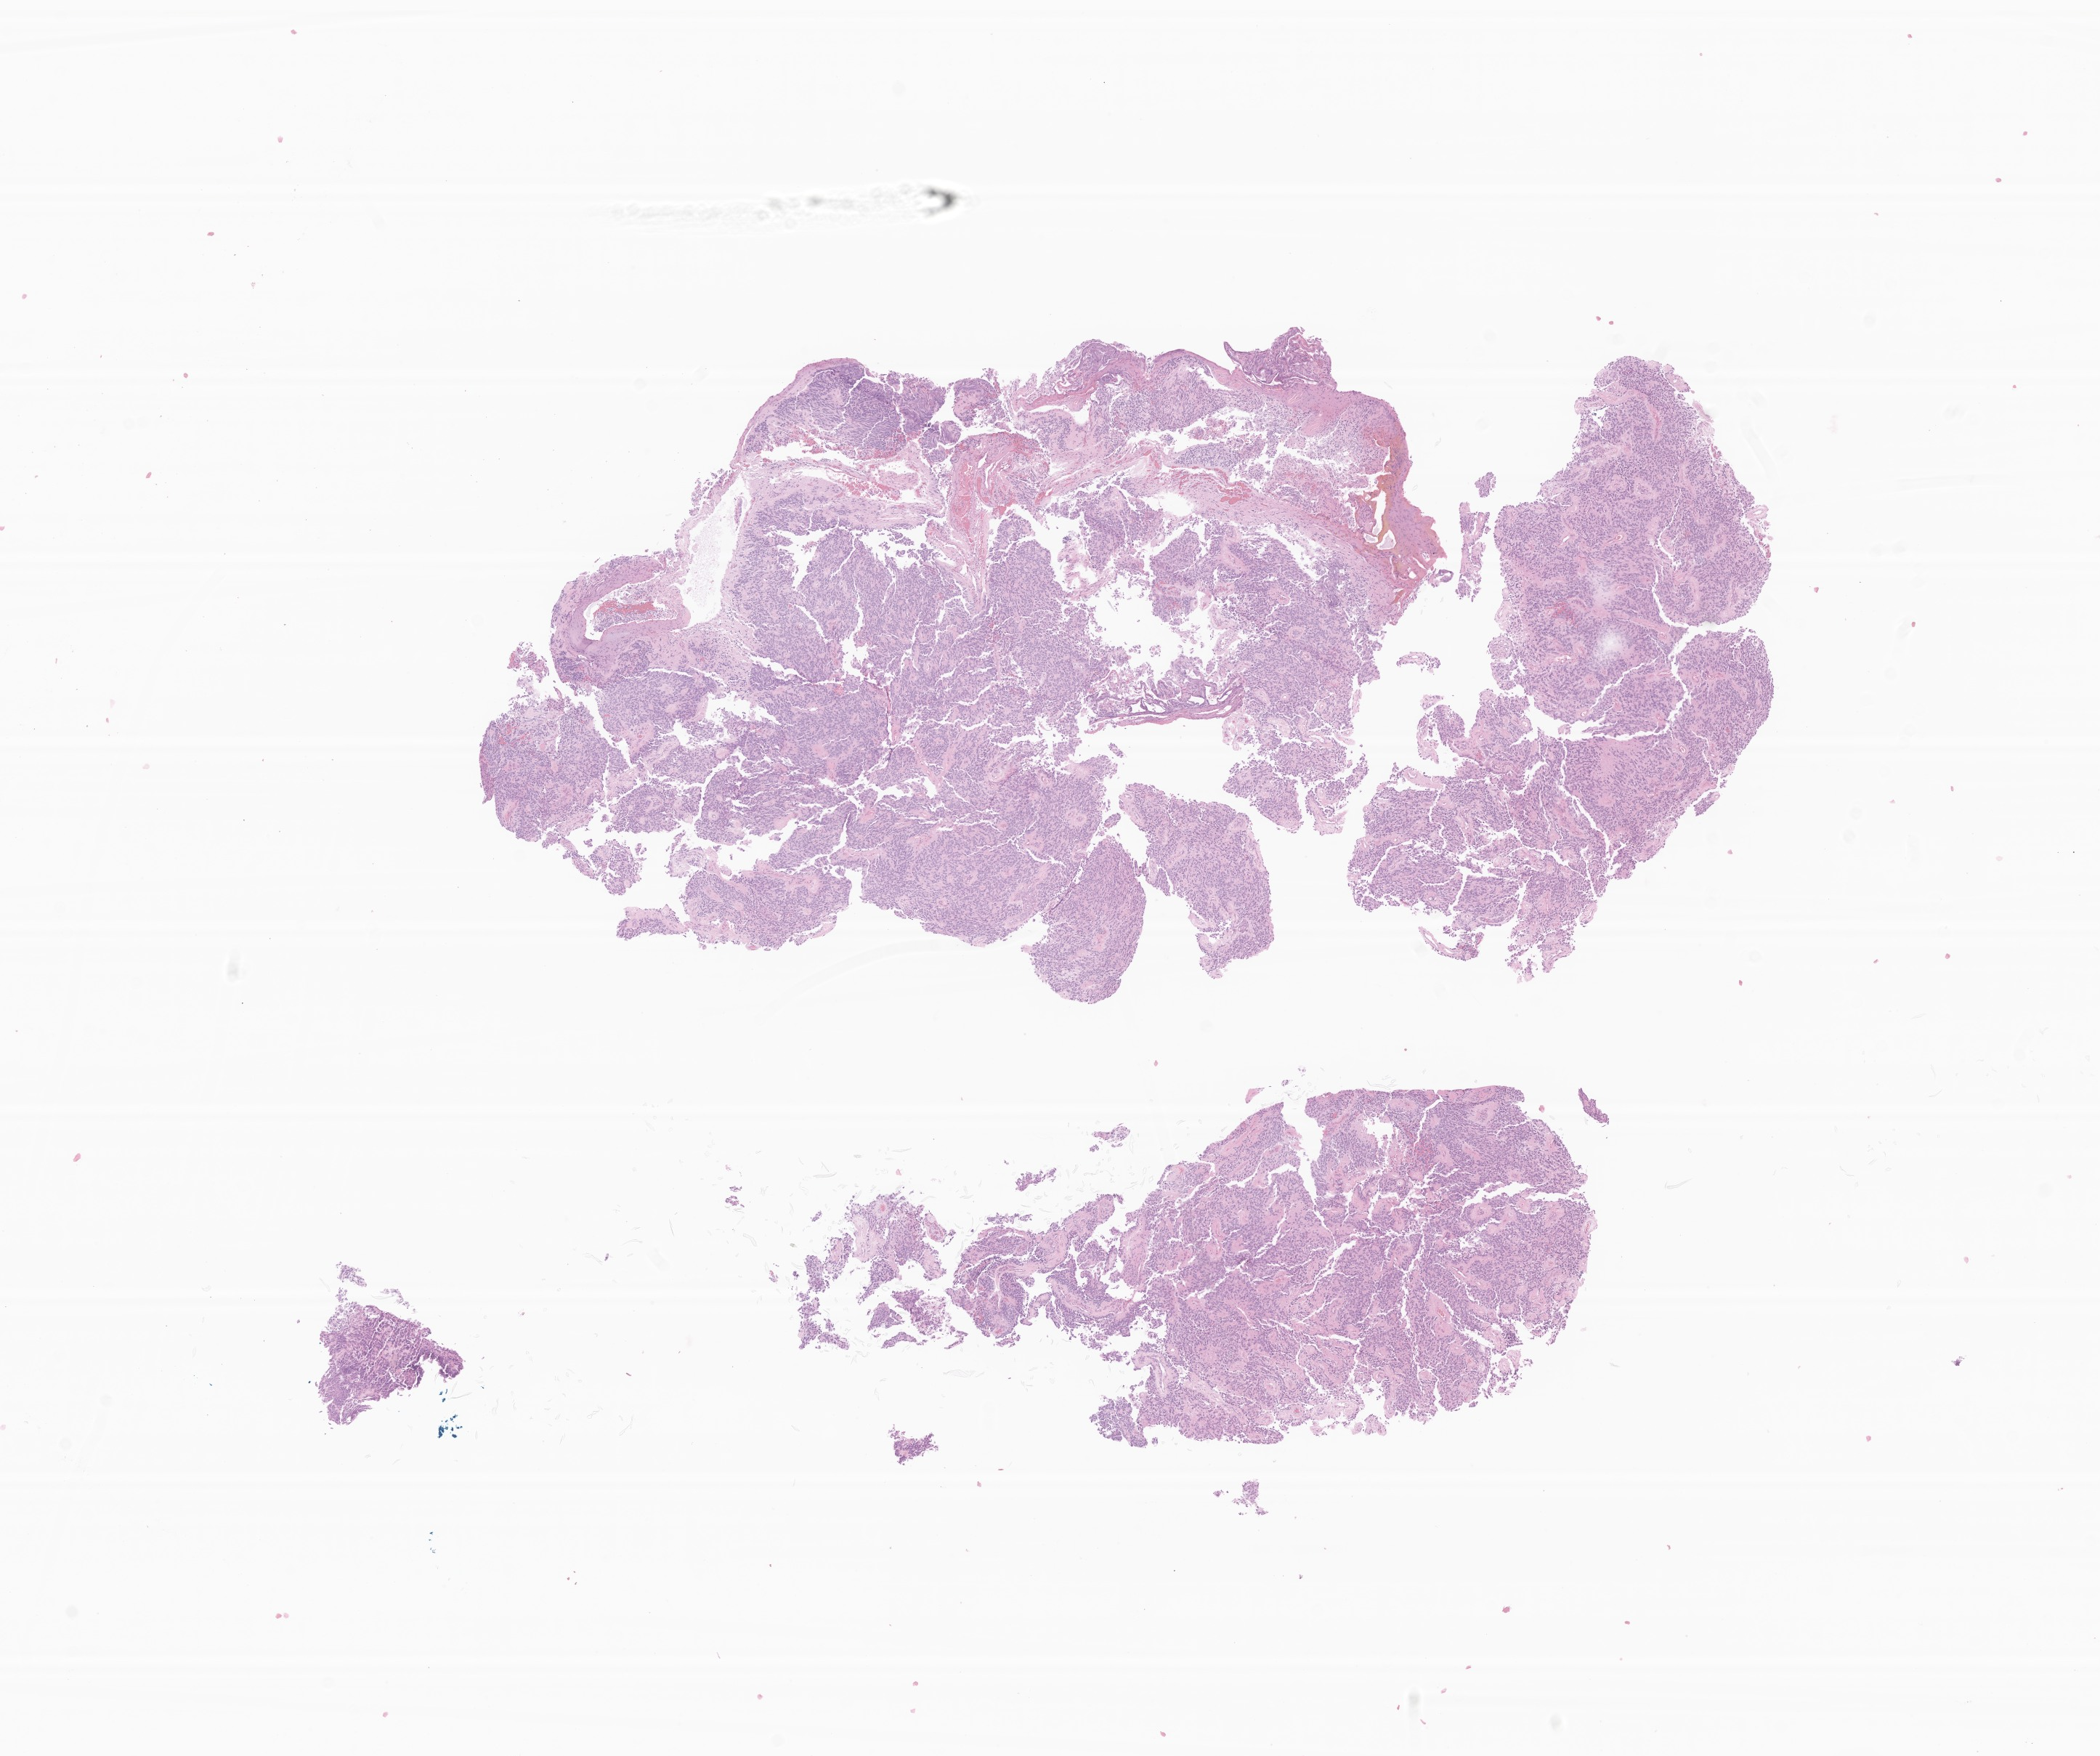
Digitized H&E-stained section of tumor tissue from the spinal cord — whole scanned area (about 12.2 x 10.2 mm) shown as a low-resolution overview, FFPE section. Male patient, age 374 days (about 1.0 years).
- diagnosis: Myxopapillary ependymoma